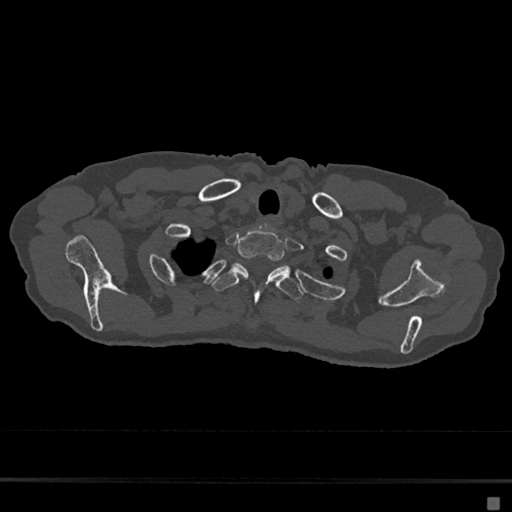
CT including the spine, one axial slice; position 592 of 797 along the scan axis; reconstruction kernel Br40s/3; 120 kVp; bone window (W 1800 / L 400 HU); 512 × 512 image matrix, field of view 360 × 360 mm. Female patient, age 68 years. Case-level facts recorded for this patient, not image findings: primary cancer: renal.
Annotated regions visible in this slice (semi-automatic segmentation, software-assisted and operator-edited):
- T1 vertebra: box from (x=236, y=229) to (x=290, y=271) px
- T2 vertebra: (x=212, y=263)–(x=304, y=305)